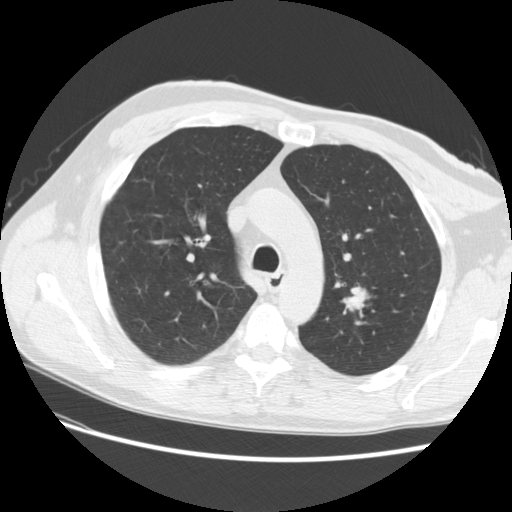
Low-dose screening chest CT, one axial slice; position 185 of 256 along the scan axis; 120 kVp; lung window (W 1500 / L -600 HU); 2.5 mm slice thickness; 512 × 512 image matrix, field of view 366 × 366 mm.
Structures marked on this image (manually delineated by an expert):
- lesion 1 (tumor, upper lobe of left lung): bounding box [x1, y1, x2, y2] px = [345, 289, 366, 309]